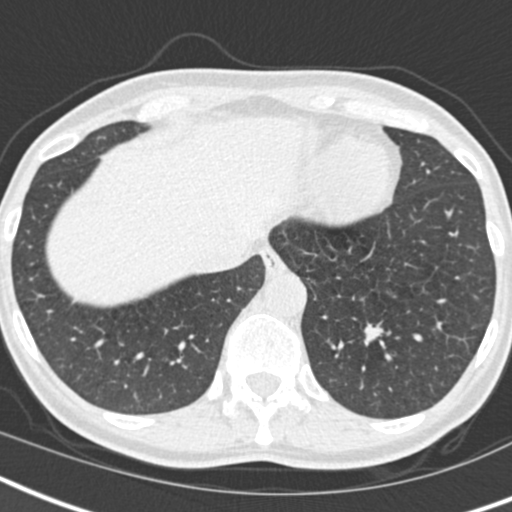
Low-dose screening chest CT, one axial slice; lung window (W 1500 / L -600 HU); 2 mm slice thickness; 512 × 512 image matrix, field of view 293 × 293 mm.
Annotated regions visible in this slice (manually delineated by an expert):
- lesion 1 (tumor, lower lobe of left lung): bounding box (x1, y1, x2, y2) in pixels: (364, 324, 383, 345)